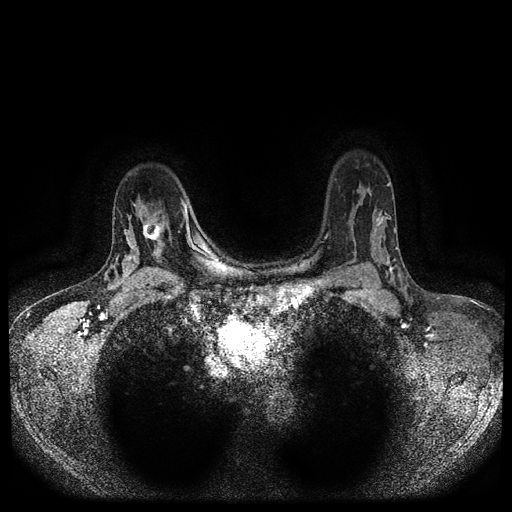
Breast MRI (dynamic contrast-enhanced, multi-phase), one axial slice. Dynamic contrast-enhanced series, time point 2 of 5 at this slice position (early post-contrast). 1.5 T. TE 2.6 ms, TR 5.4 ms. 2 mm slice thickness. 512 × 512 image matrix, field of view 340 × 340 mm. Patient: female, 47 years.
Outlined on this slice (semi-automatically segmented with operator editing):
- breast lesion (labelled 'tumour' in the annotation; benign lesions carry a separate 'benign' label): bounding box [x1, y1, x2, y2] px = [140, 220, 164, 243]